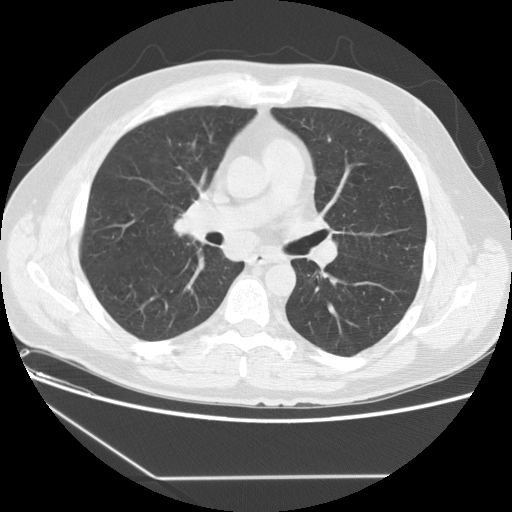
Low-dose screening chest CT, one axial slice. Slice 84 of 154 in the series (ordered by position). Reconstruction kernel STANDARD. 120 kVp. Lung window (W 1500 / L -600 HU). 2.5 mm slice thickness. 512 × 512 image matrix, field of view 370 × 370 mm.
Structures marked on this image (expert manual segmentation):
- lesion 1 (tumor, middle lobe of right lung): box from (x=174, y=216) to (x=198, y=235) px